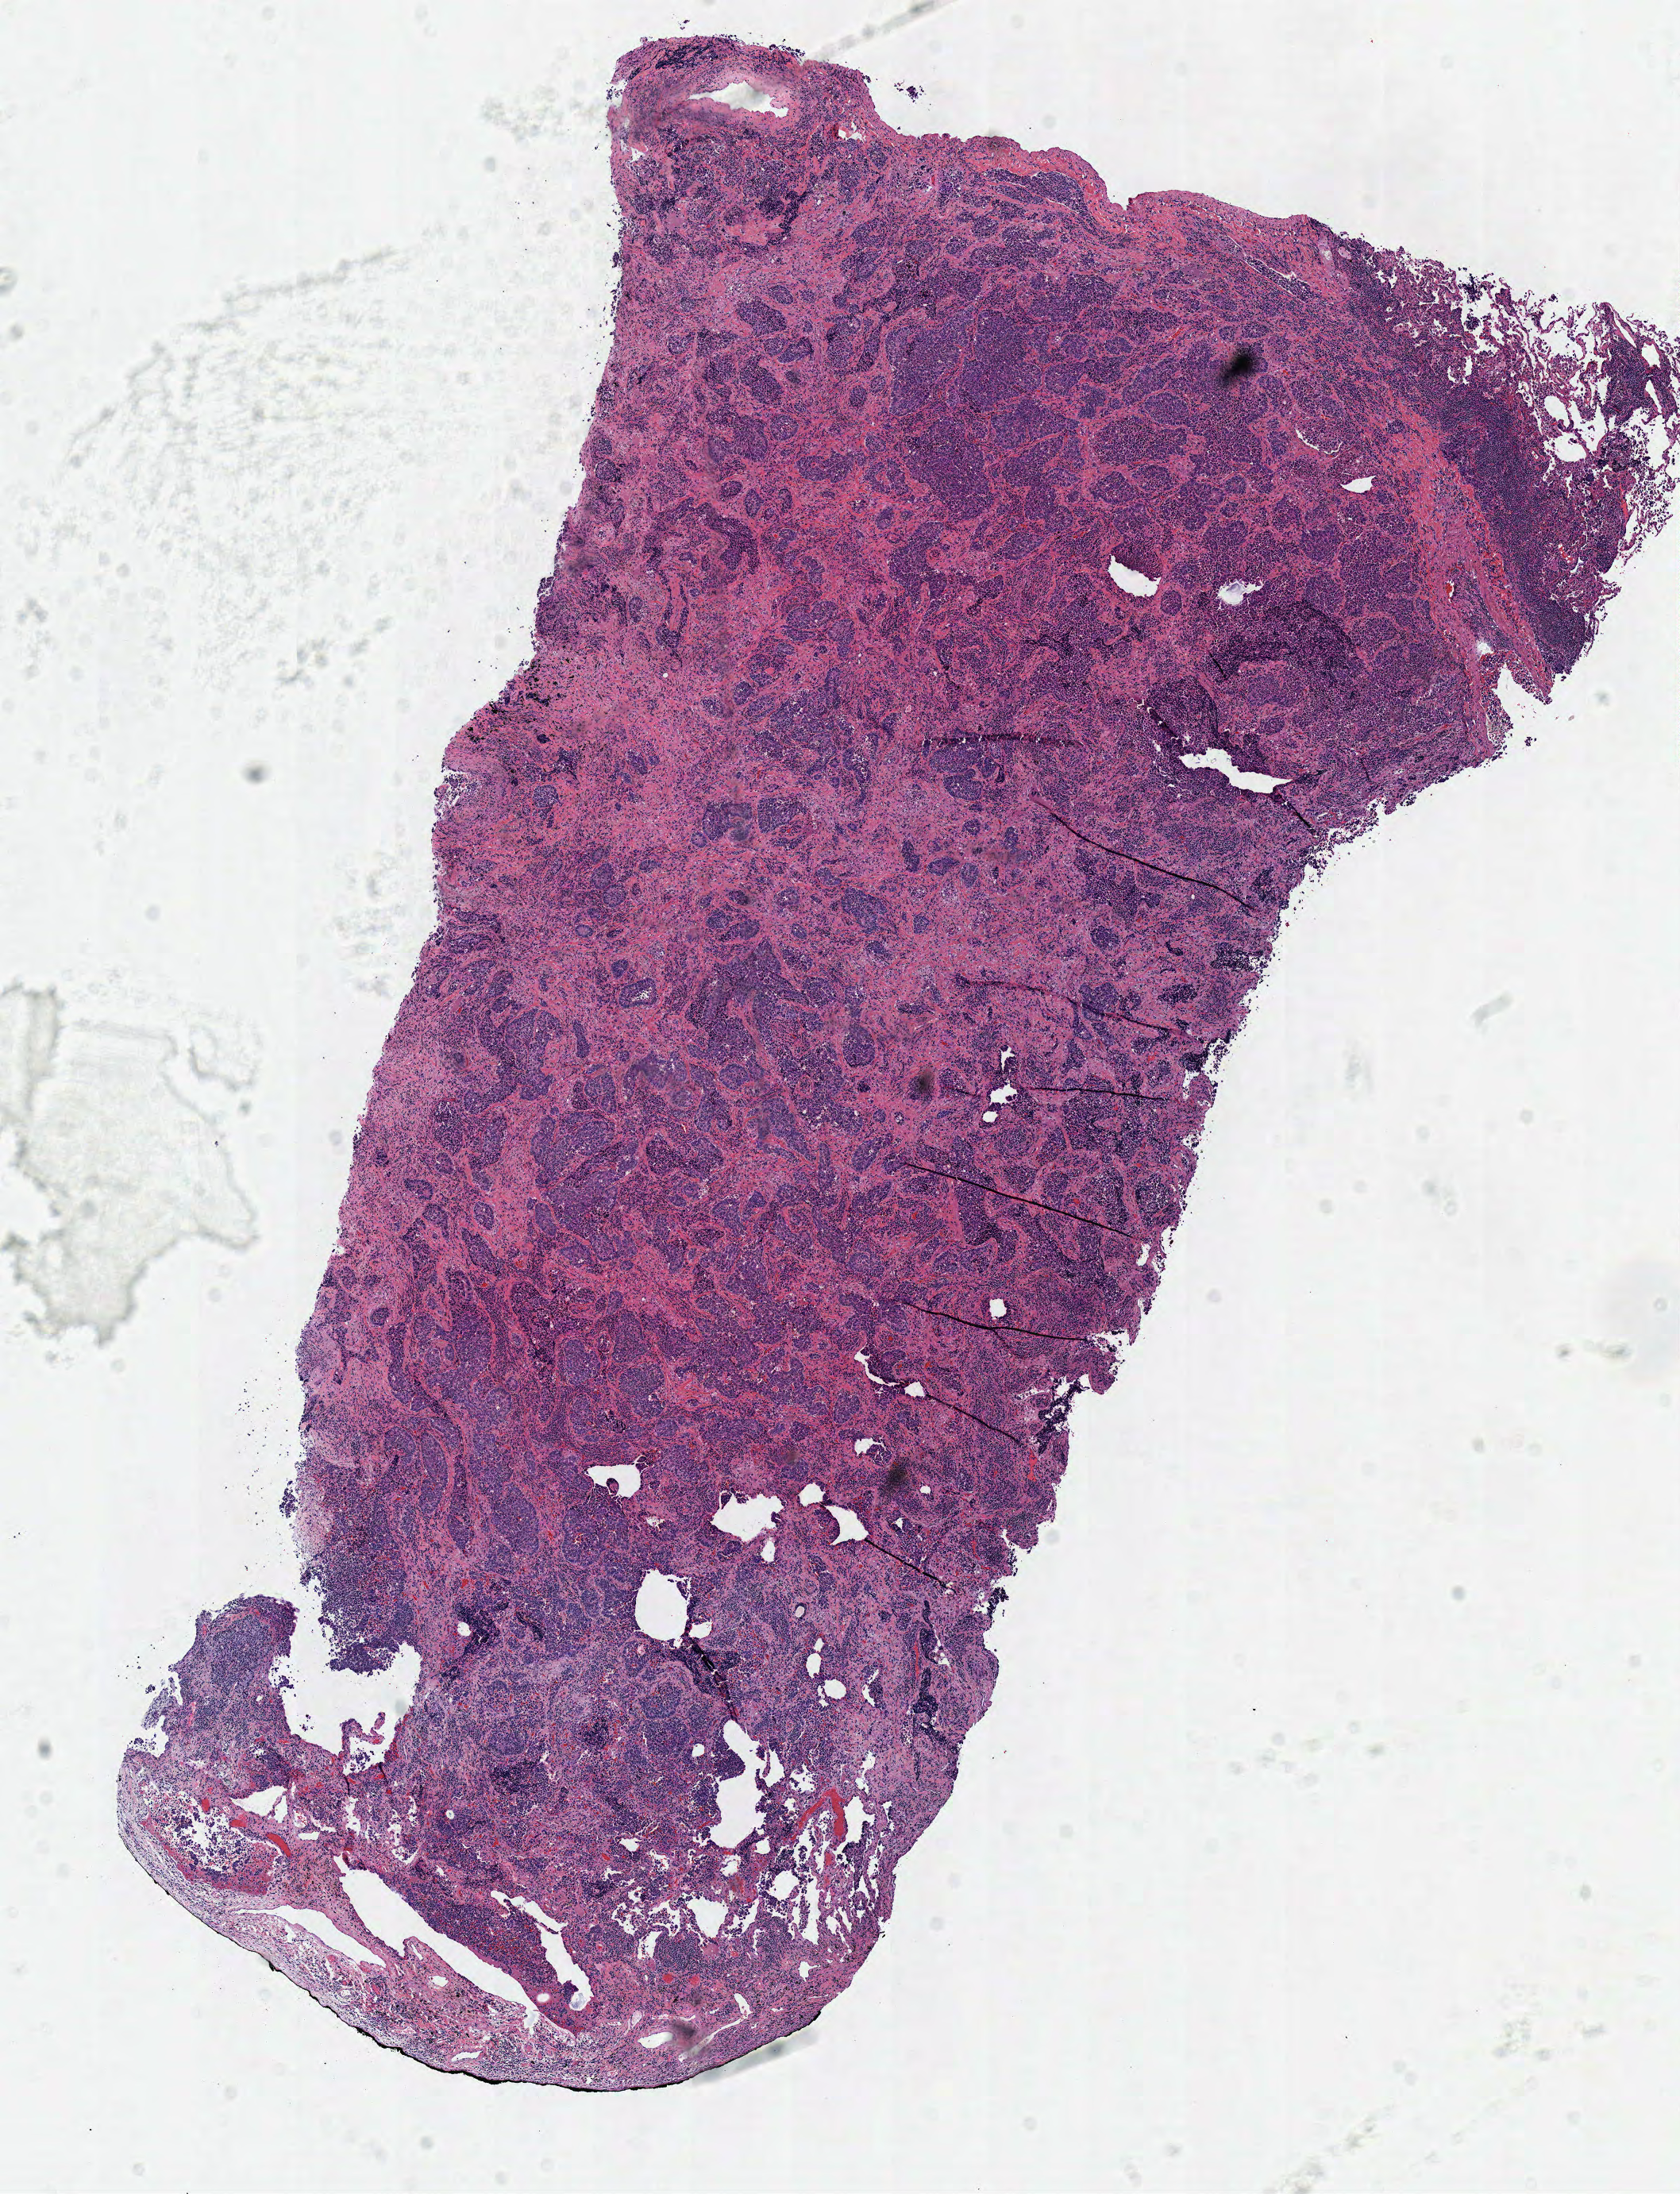
Whole-slide histology image, Hematoxylin and eosin (H&E) stained — shown as a low-resolution overview of the whole scanned area (about 8.3 x 10.9 mm, from a 40x scan); frozen section from the top of the tissue portion; sample: primary tumour, lung. Male, age 59 years at initial diagnosis. Pathologist review of this section (percent, as recorded): tumour cells 90%, tumour nuclei 80%, normal cells 10%, stromal cells 0%, necrosis 0%. Infiltration values recorded for this section: lymphocyte infiltration 10%, monocyte infiltration 0%, neutrophil infiltration 0%.
- AJCC pathologic stage: IA (6th edition)
- histologic diagnosis: Adenocarcinoma, NOS